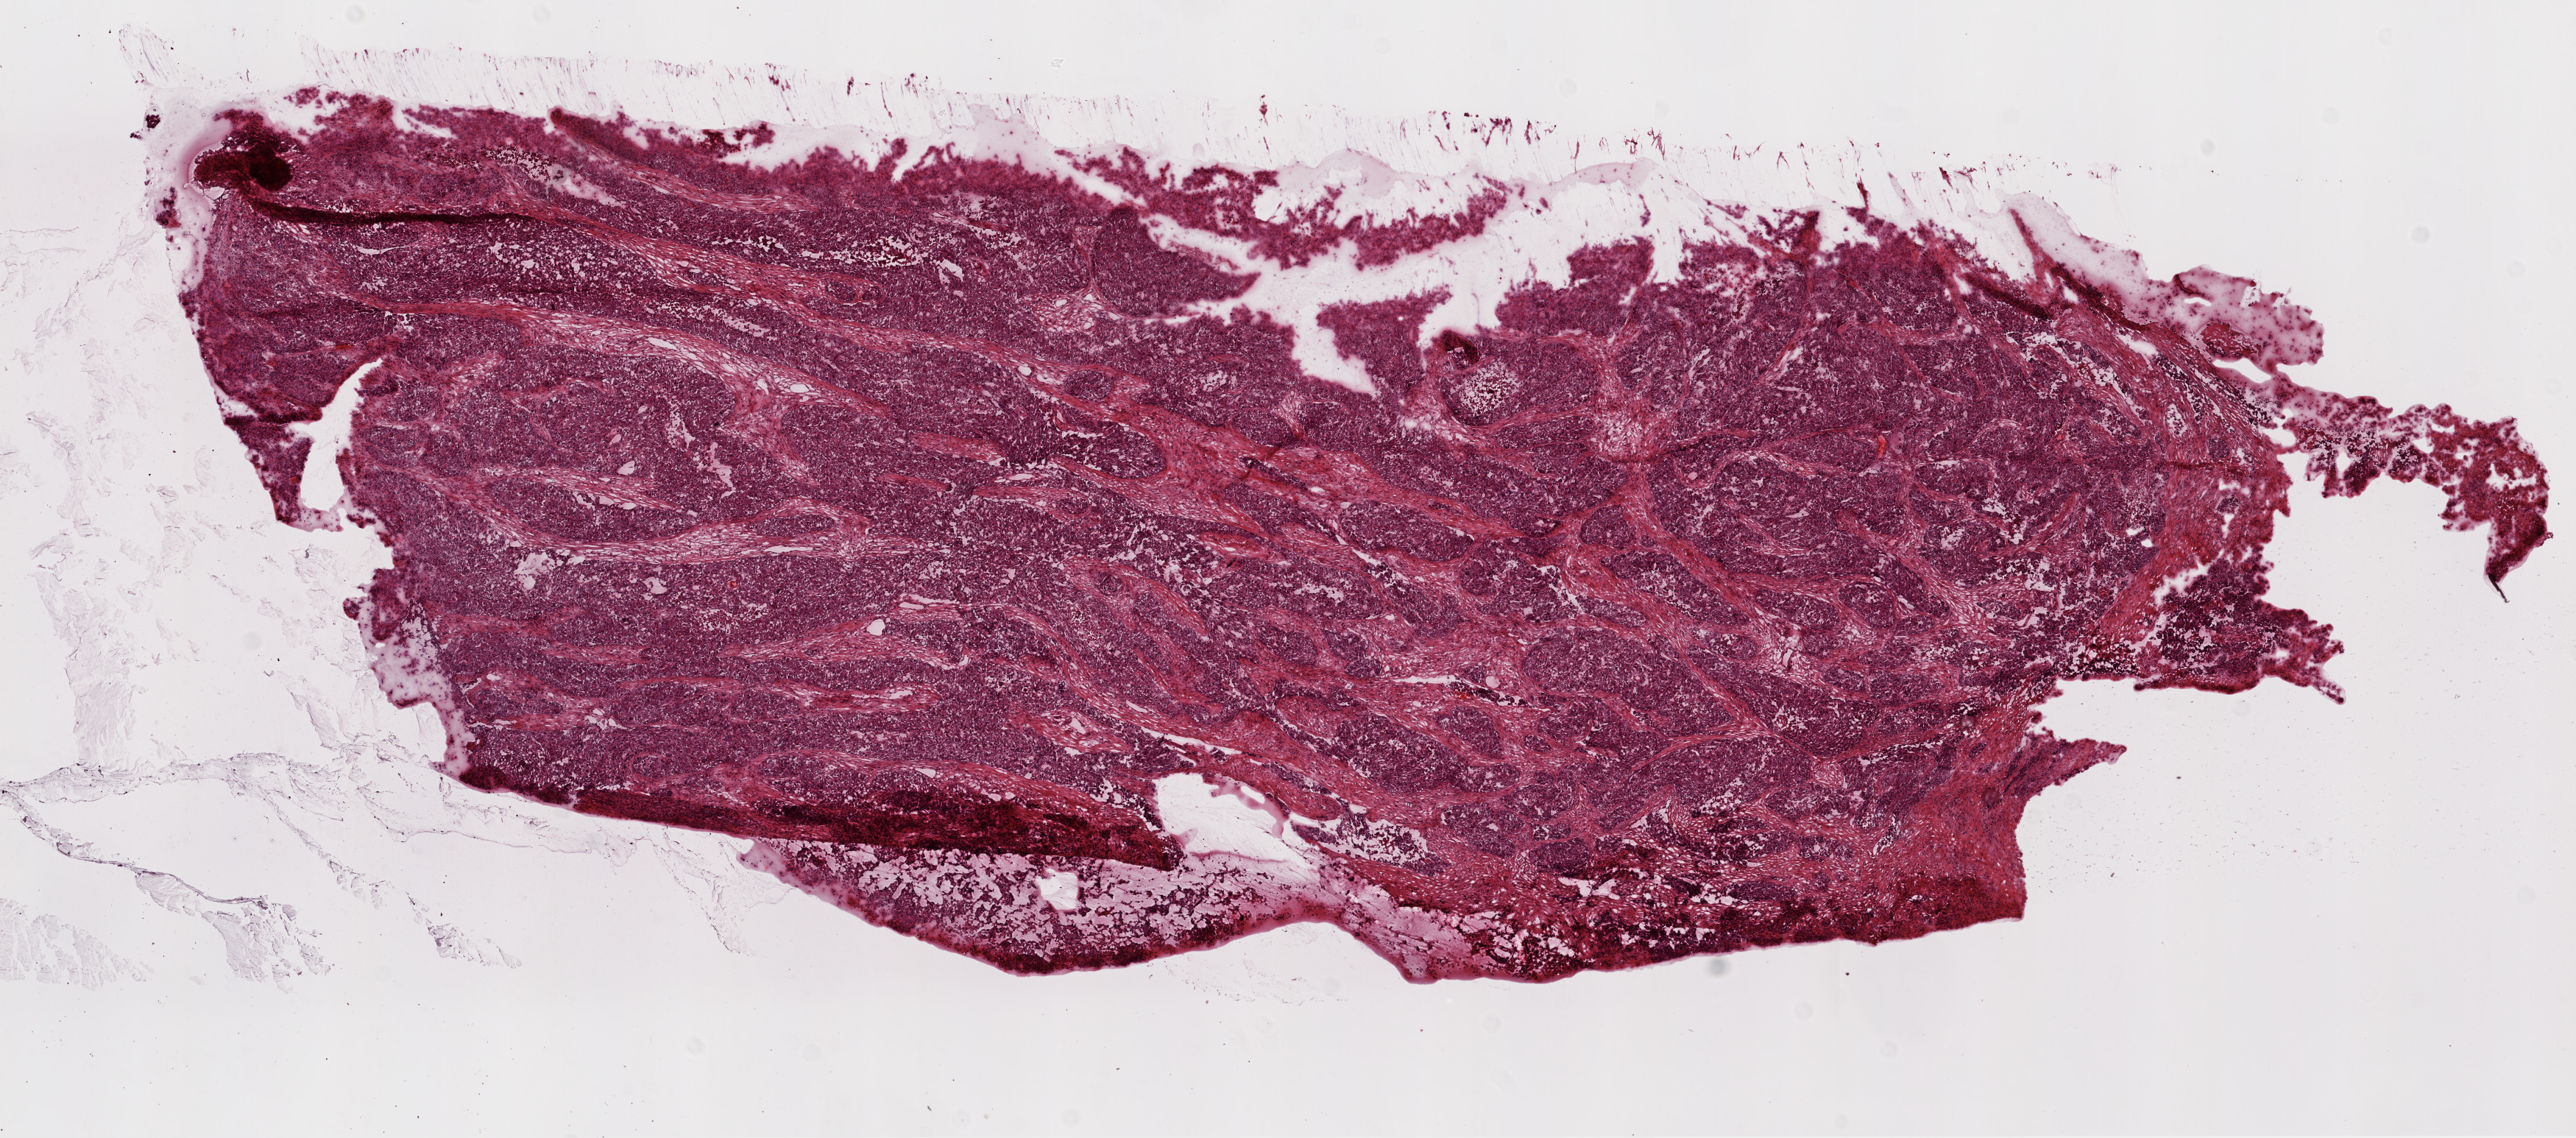
Hematoxylin and eosin (H&E) stained whole-slide image — low-resolution overview of the scanned area, about 14.0 x 6.2 mm. Frozen section. Ovary, primary tumour sample. Female, age 49 years at initial diagnosis. Histologic grade: G3 (poorly differentiated). Composition of this section per pathologist review: tumour cells 85%, tumour nuclei 85%, normal cells 0%, stromal cells 15%, necrosis 0%. Inflammatory infiltration, as recorded: lymphocyte infiltration 0%, monocyte infiltration 0%, neutrophil infiltration 0%.
FIGO stage: IIIC. Diagnosis: Serous cystadenocarcinoma, NOS.